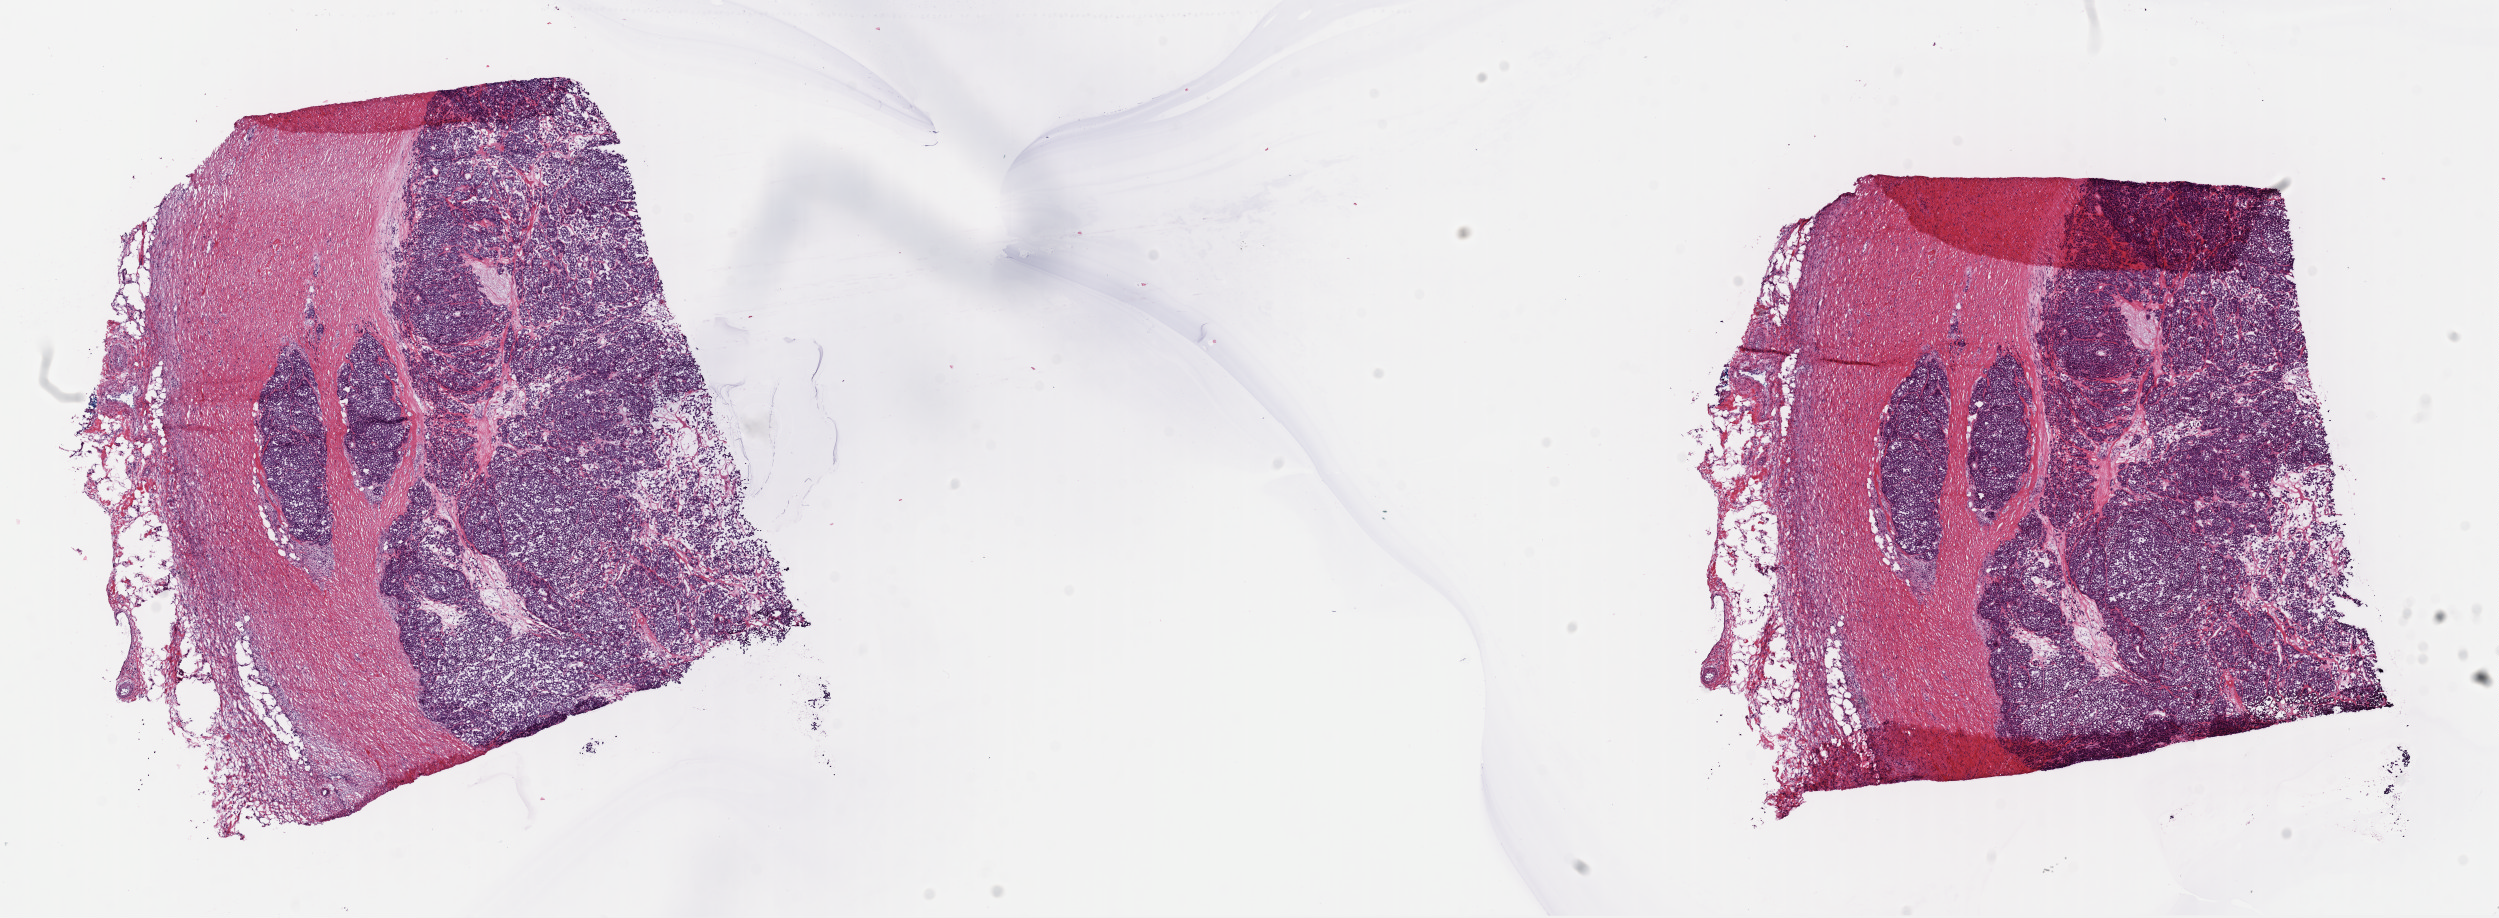
Whole-slide histology image, H&E-stained, whole scanned area (about 19.7 x 7.2 mm) shown as a low-resolution overview. Frozen section from the top of the tissue portion. Metastatic tumour sample, sampled site not recorded. Male patient; age at initial diagnosis 68 years. Pathologist review of this section (percent, as recorded): tumour cells 80%, tumour nuclei 80%, normal cells 0%, stromal cells 20%, necrosis 0%. Infiltration values recorded for this section: lymphocyte infiltration 3%, monocyte infiltration 1%, neutrophil infiltration 0%.
This section: metastatic tumour tissue. Patient diagnosis: Malignant melanoma, NOS.